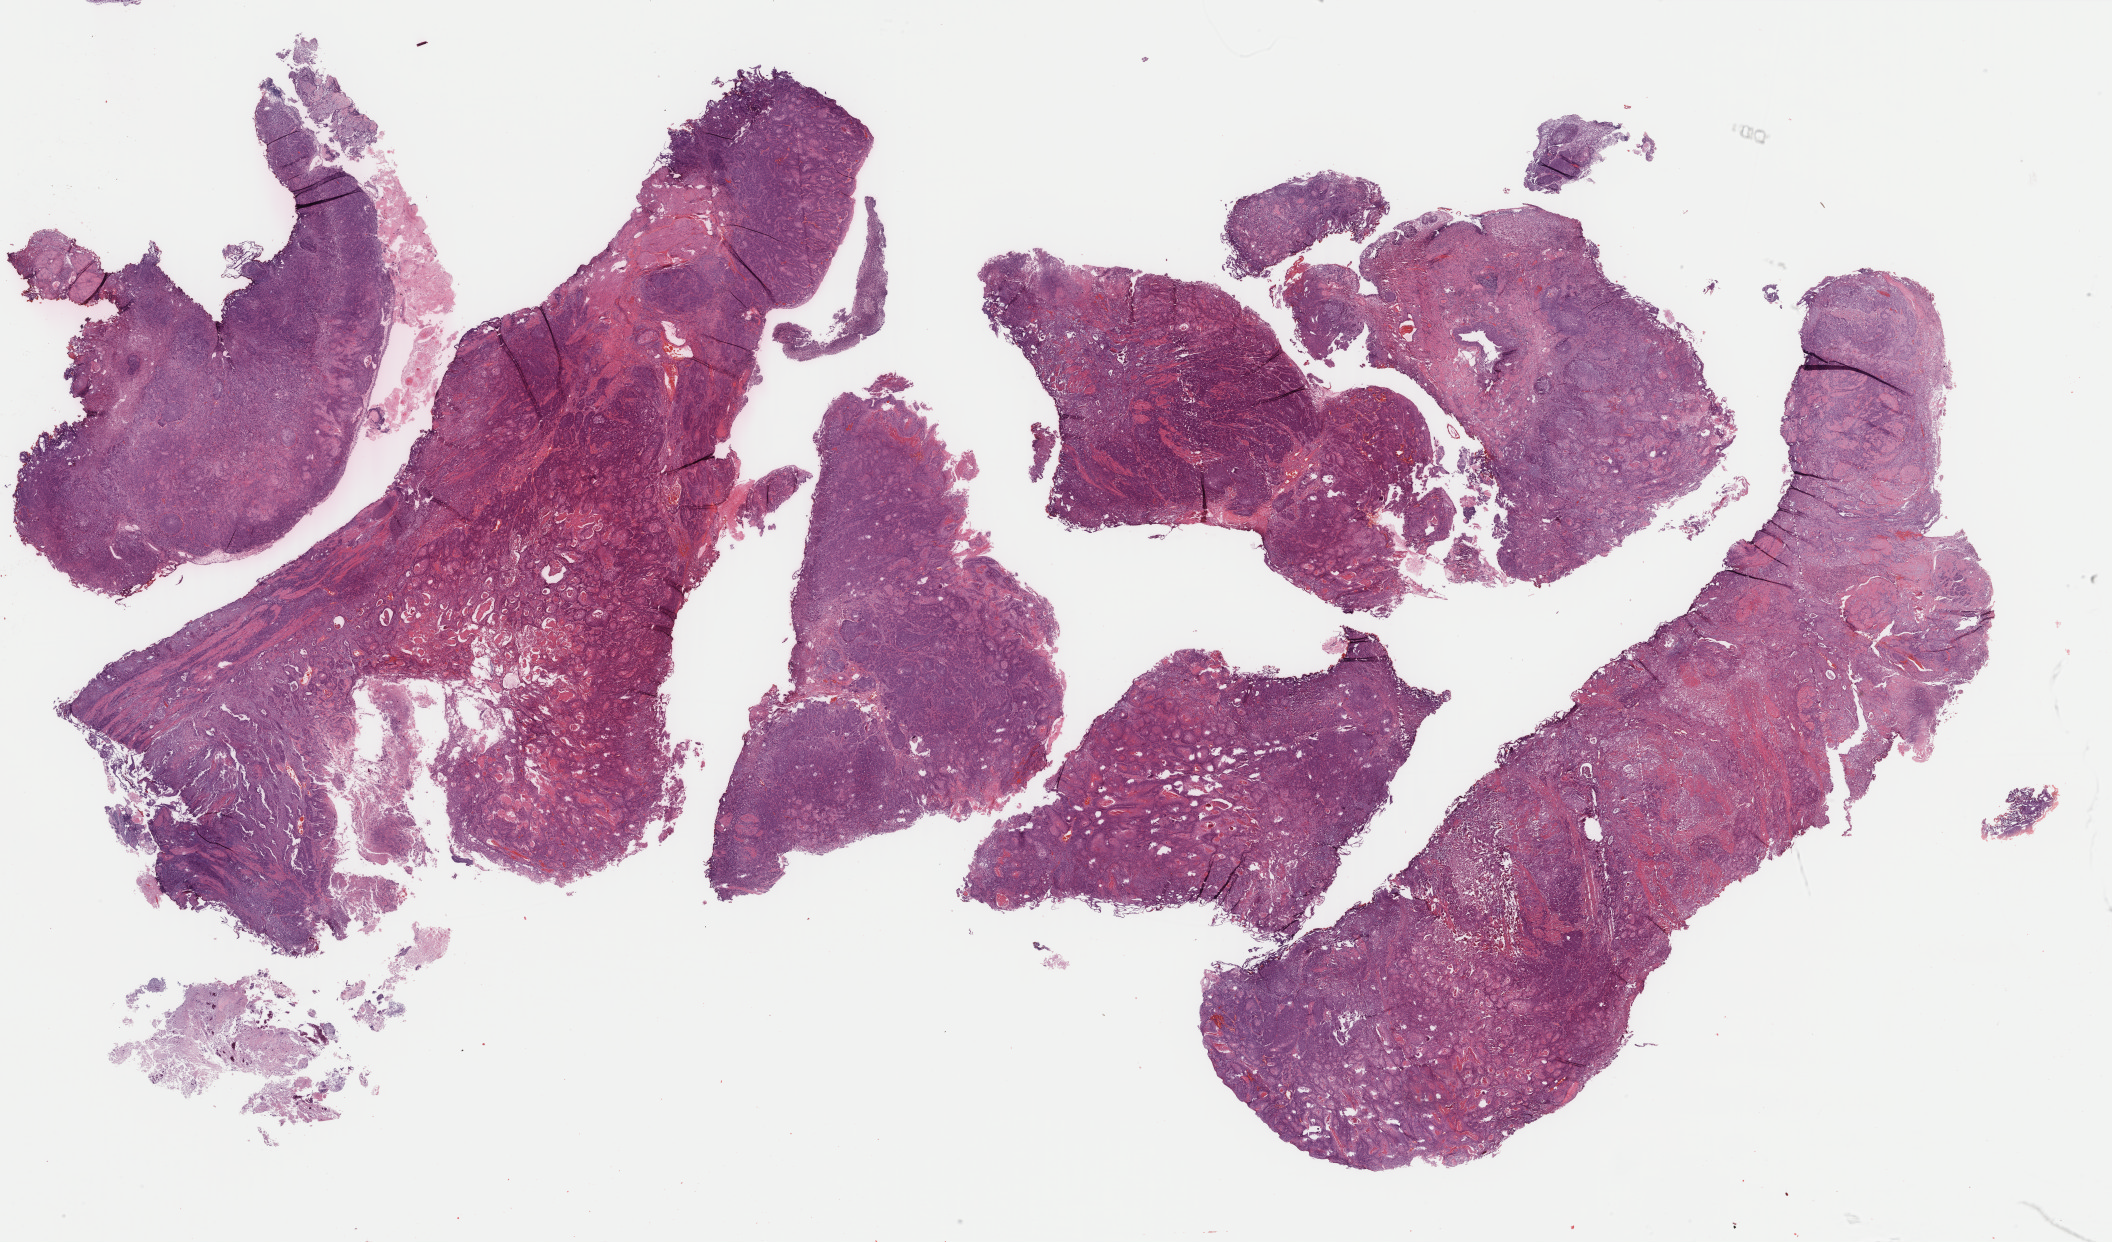
H&E whole-slide image, whole scanned area (about 33.5 x 19.7 mm, from a 40x scan) shown as a low-resolution overview, formalin-fixed paraffin-embedded (FFPE) diagnostic section, sample: primary tumour, bladder. Male, age 66 years at initial diagnosis. Histologic grade: high grade.
AJCC pathologic stage: II (6th edition). TNM: NX MX. Histologic diagnosis: Transitional cell carcinoma.